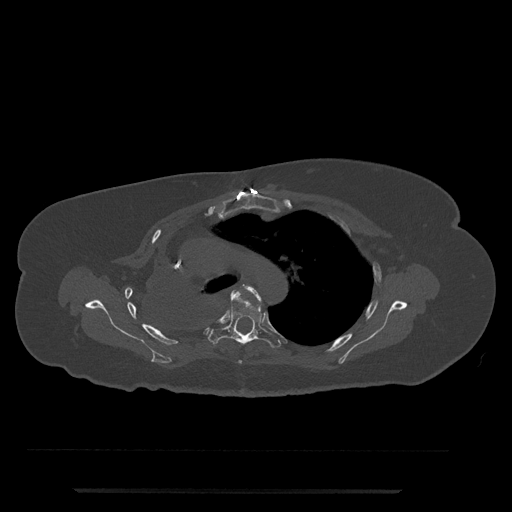
CT including the spine, one axial slice; slice 553 of 797 in the series (ordered by position); reconstruction kernel Br40s/3; bone window (W 1800 / L 400 HU); 512 × 512 image matrix, field of view 440 × 440 mm. Patient: female, 51 years. Case-level facts recorded for this patient, not image findings: primary cancer: neuro.
Outlined on this slice (semi-automatically segmented with operator editing):
- T4 vertebra: bounding box (x1, y1, x2, y2) in pixels: (238, 286, 261, 364)
- T5 vertebra: (208, 290, 281, 348)